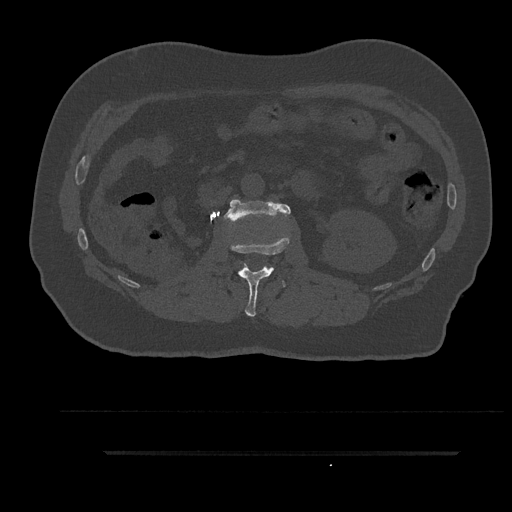
CT including the spine, one axial slice; slice 153 of 797 in the series (ordered by position); bone window (W 1800 / L 400 HU); 0.5 mm slice thickness; 512 × 512 image matrix, field of view 432 × 432 mm. Male patient, age 63 years. From the clinical record (not read from this slice): primary cancer: renal.
Structures marked on this image (semi-automatic segmentation, software-assisted and operator-edited):
- L1 vertebra: box from (x=230, y=235) to (x=289, y=317) px
- L2 vertebra: (x=224, y=199)–(x=291, y=222)